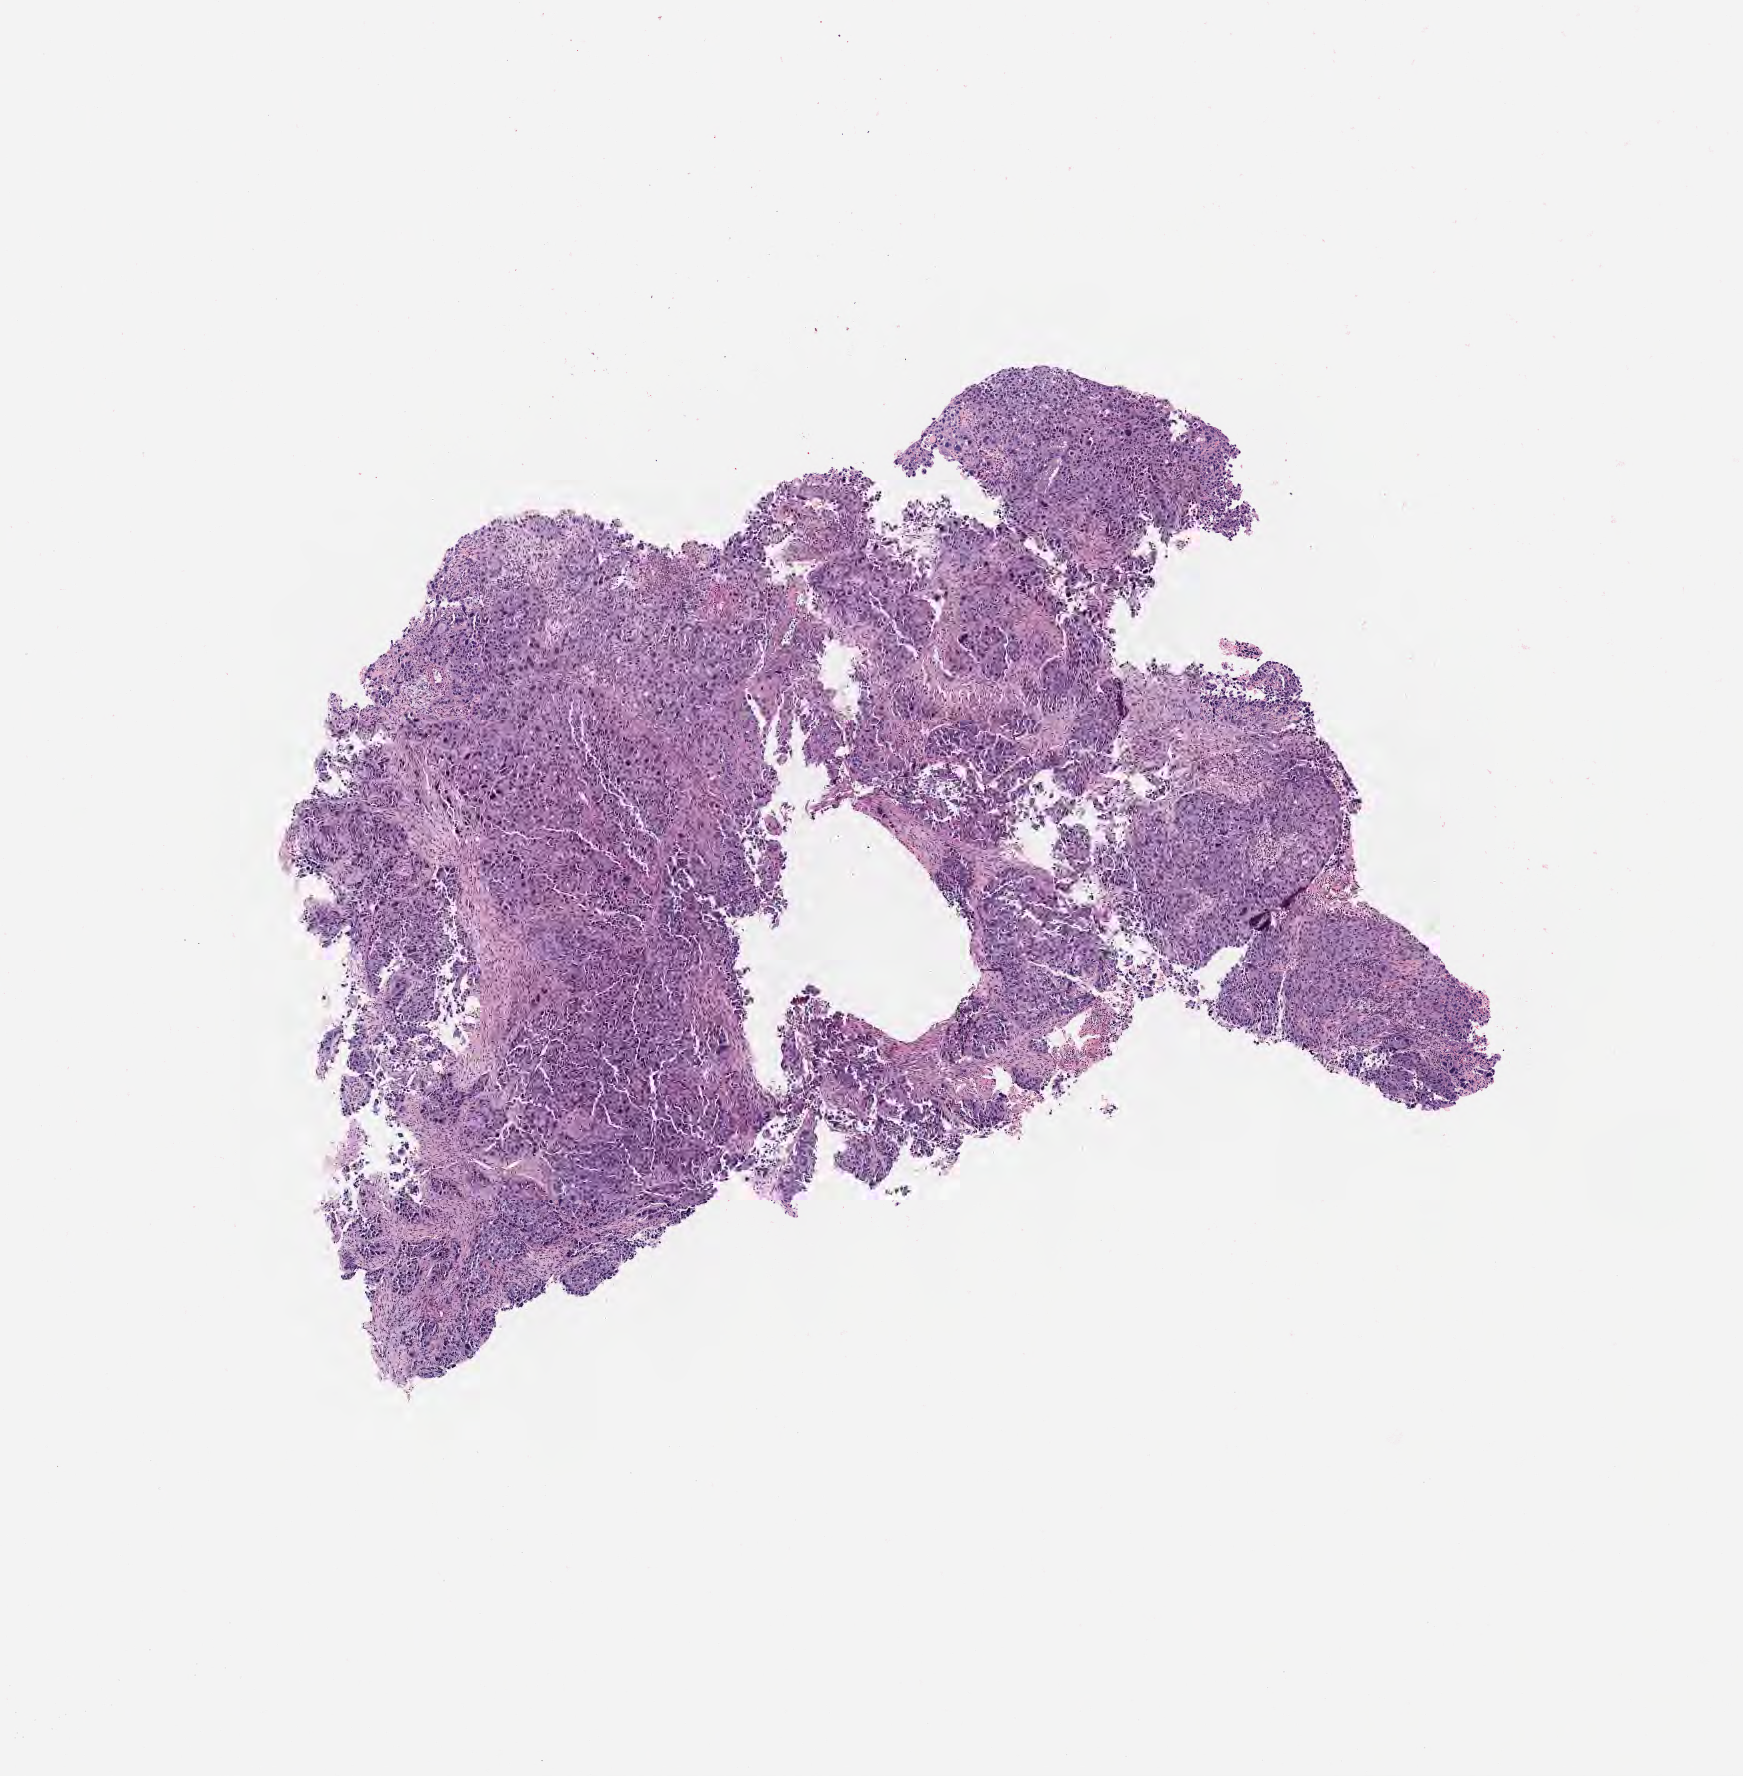
Digitized hematoxylin and eosin (H&E)-stained section, a low-resolution overview of the entire scanned area, about 7.0 x 7.2 mm, specimen: tumor tissue, site: cervix. Patient female; age 43 years.
Histologic diagnosis: Squamous cell carcinoma, large cell, nonkeratinizing, NOS.